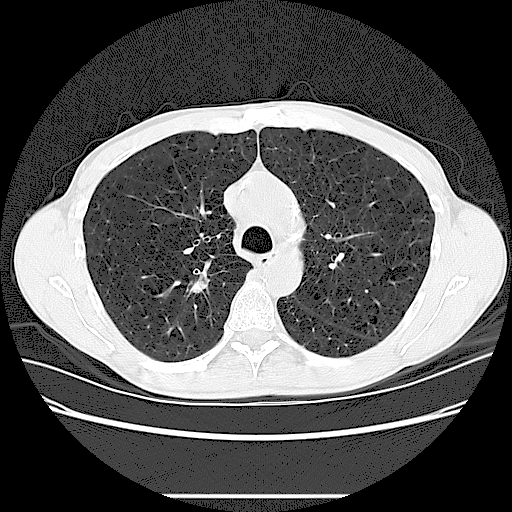
Chest CT (low-dose screening protocol), one axial image. Second screening round (one year after baseline). Lung window (W 1500 / L -600 HU). 2.5 mm slice thickness. Slice 41 of 131 in the series. Male, age 59 years at enrolment. Current smoker at enrolment.
Expert-annotated lung lesion, bounding box (x1, y1, x2, y2) in pixels: (176, 268, 219, 311). The exam's reader record, not a measurement of the box and not confirmed to be the same lesion: non-calcified nodule or mass ≥4 mm, right upper lobe, 7 × 4 mm, smooth margins, soft tissue attenuation, pre-existing on the prior screen: no. Later outcome: lung cancer diagnosed 69 days after this screen — squamous cell carcinoma, NOS, right upper lobe, stage IIIA (AJCC 6th edition), 7 mm at pathology.